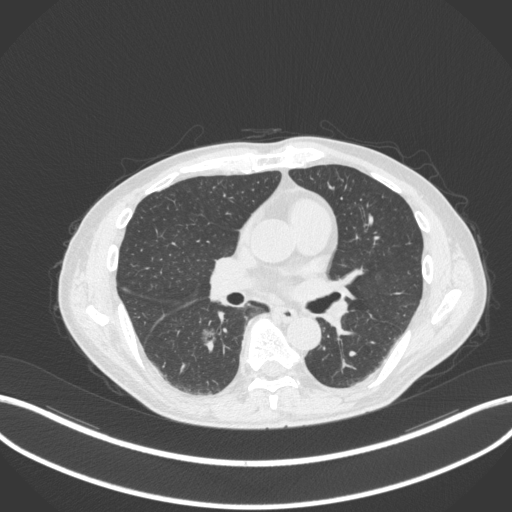
Chest CT, one axial slice. Slice 170 of 324 in the series (ordered by position). Reconstruction kernel B31f. 120 kVp. Lung window (W 1500 / L -600 HU). 1 mm slice thickness. 512 × 512 image matrix, field of view 400 × 400 mm. Patient: male, 61 years. From the clinical record (not read from this slice): clinical TNM (as recorded): T1c N0 M0.
Structures marked on this image (bounding box drawn by a radiologist):
- lung tumour (recorded histology: adenocarcinoma): bounding box [x1, y1, x2, y2] px = [197, 320, 218, 354]